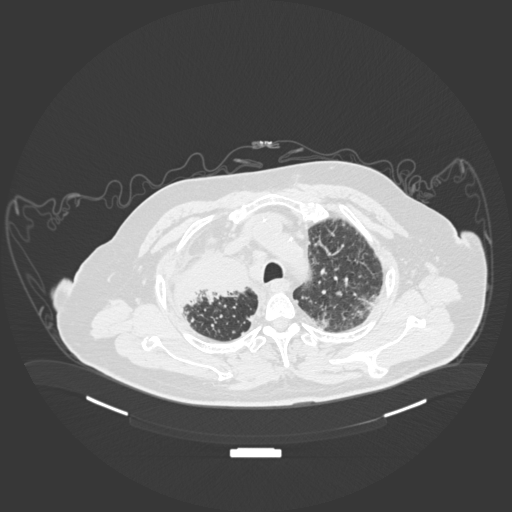
Chest CT, one axial slice. Position 151 of 201 along the scan axis. Reconstruction kernel B30f. 120 kVp. Lung window (W 1500 / L -600 HU). 1 mm slice thickness. 512 × 512 image matrix, field of view 500 × 500 mm. Male patient, age 69 years. From the clinical record (not read from this slice): clinical TNM (as recorded): T4 N3 M1.
Outlined on this slice (rectangle marked by the reading radiologist):
- lung tumour (recorded histology: adenocarcinoma): bounding box <172,250,259,318> (left, top, right, bottom; pixels)